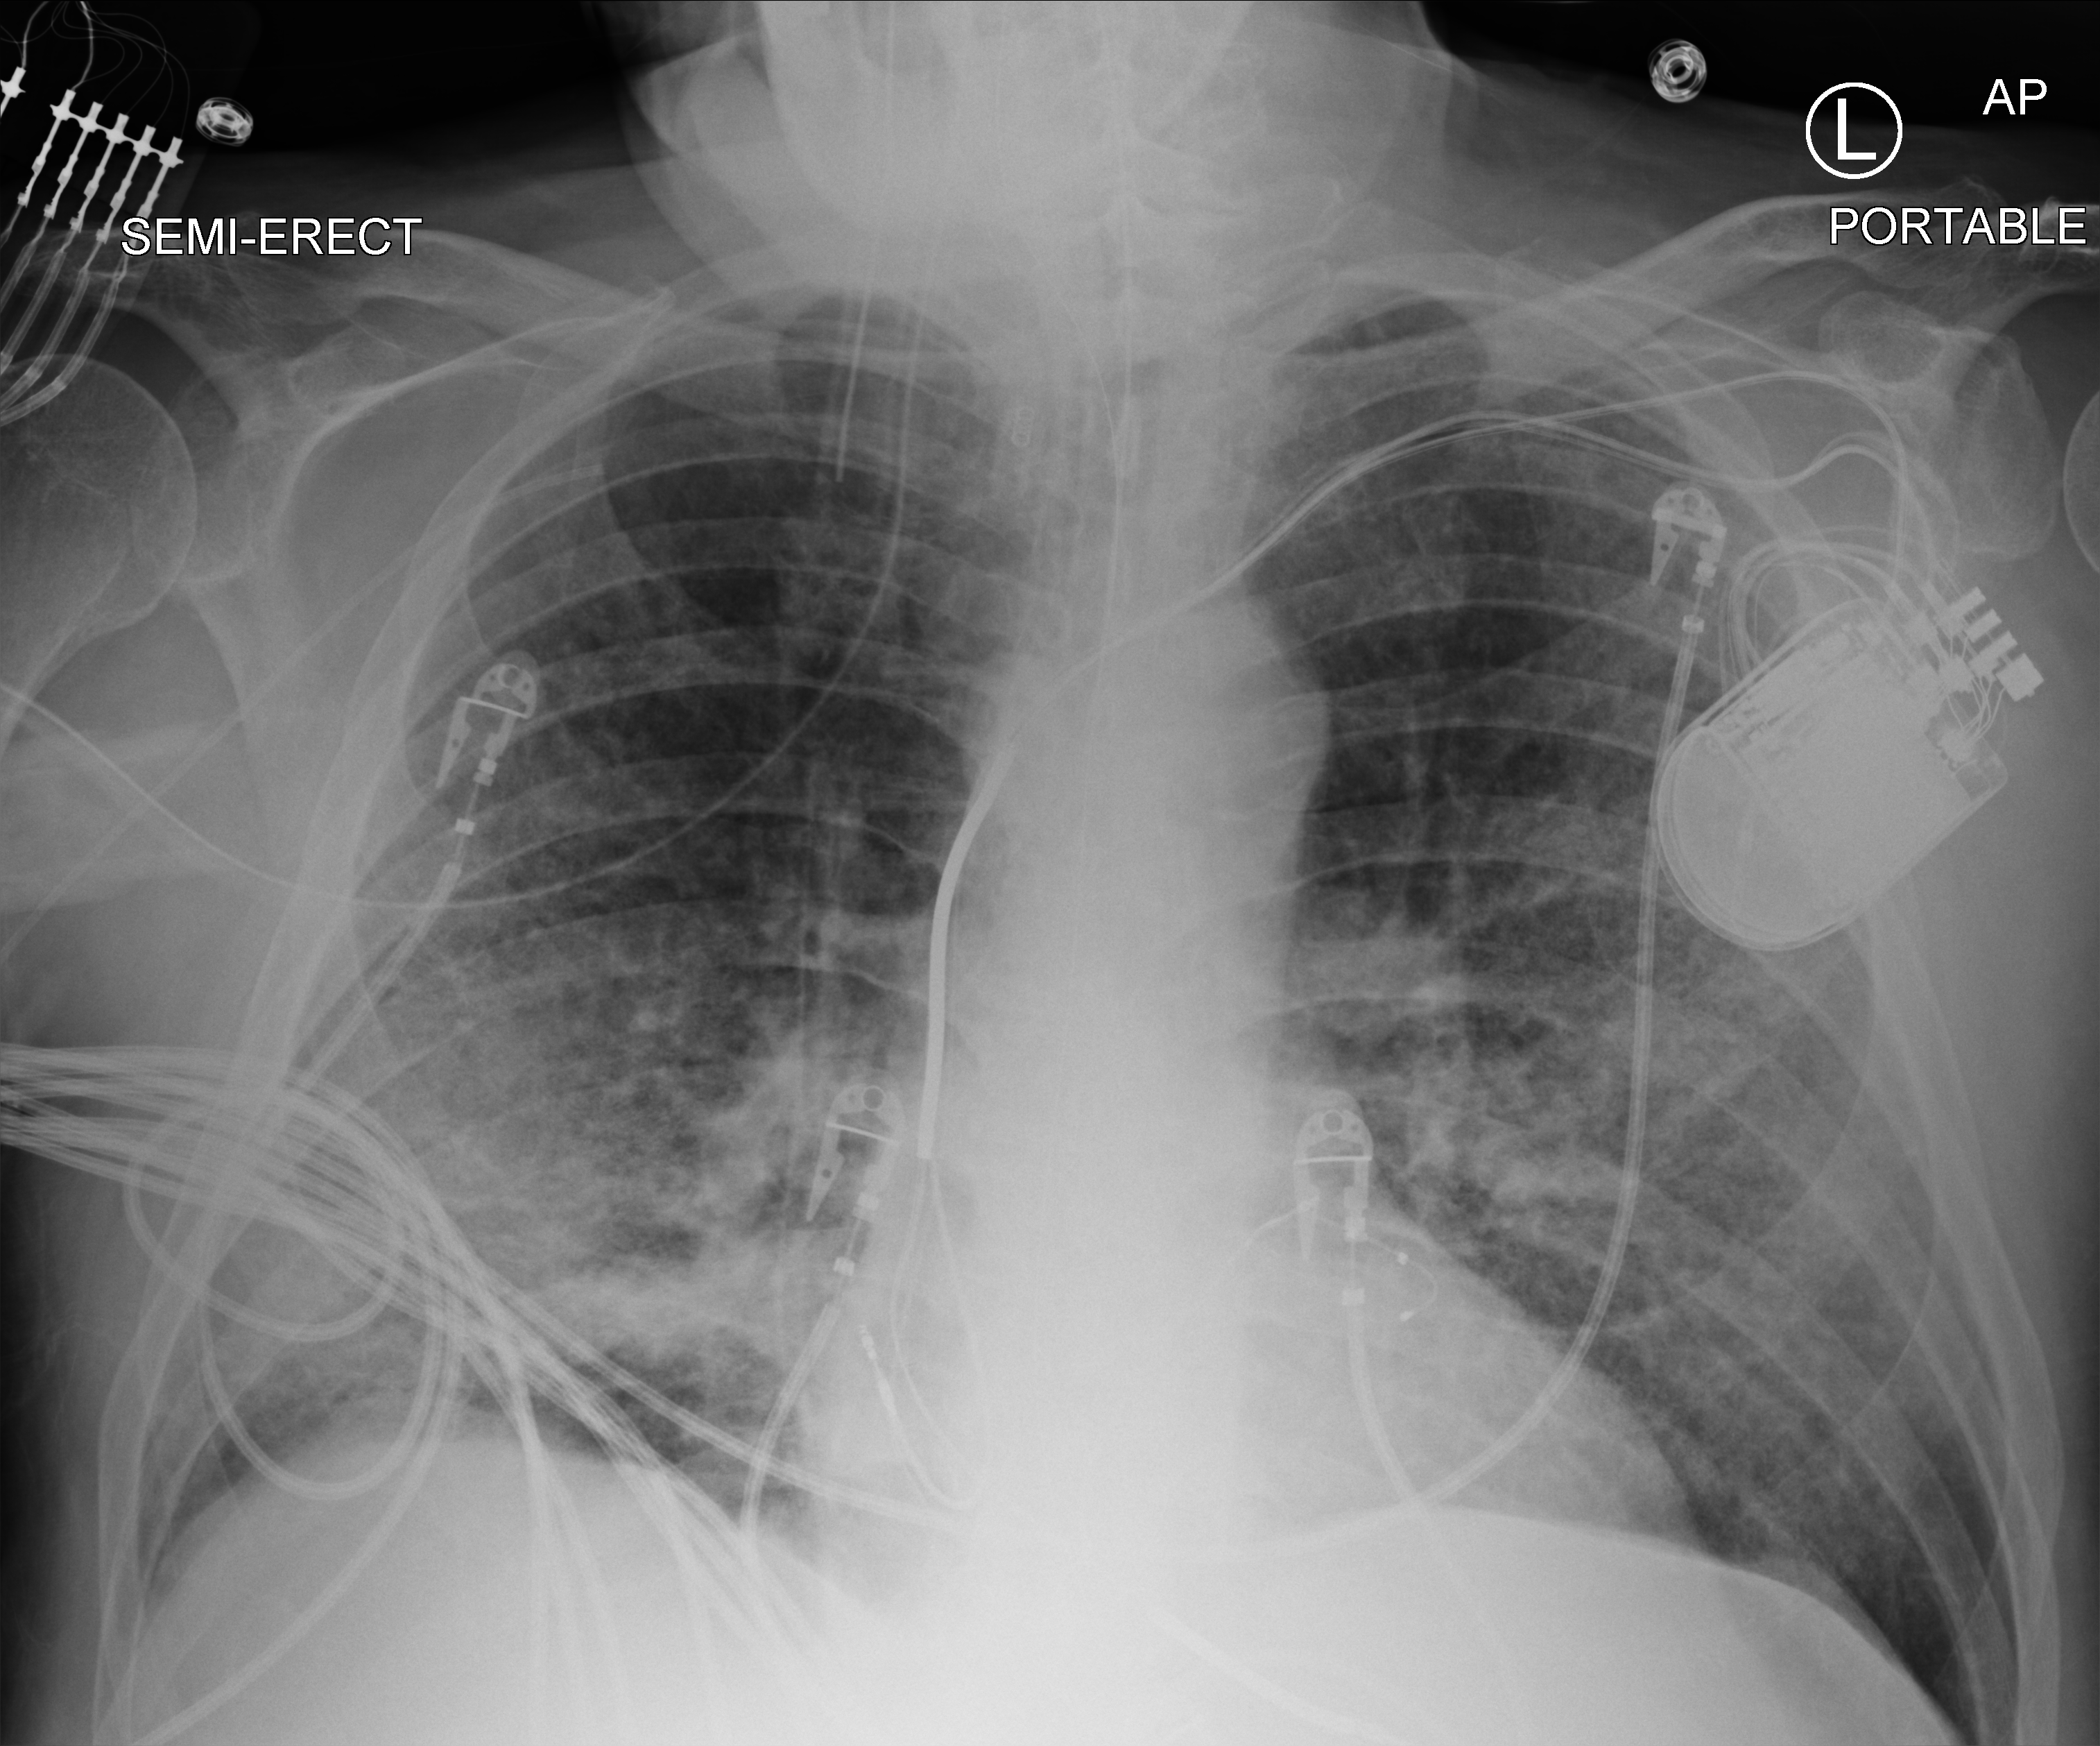
Chest X-ray (portable); anteroposterior (AP) projection. Patient hospitalised with COVID-19; male, aged 60–74 years.
Admission-level facts for this patient (not findings on this image; timing relative to this image not recorded): mechanically ventilated during this hospital stay: yes; smoking status (admission record): former; admitted to intensive care during this hospital stay: yes.